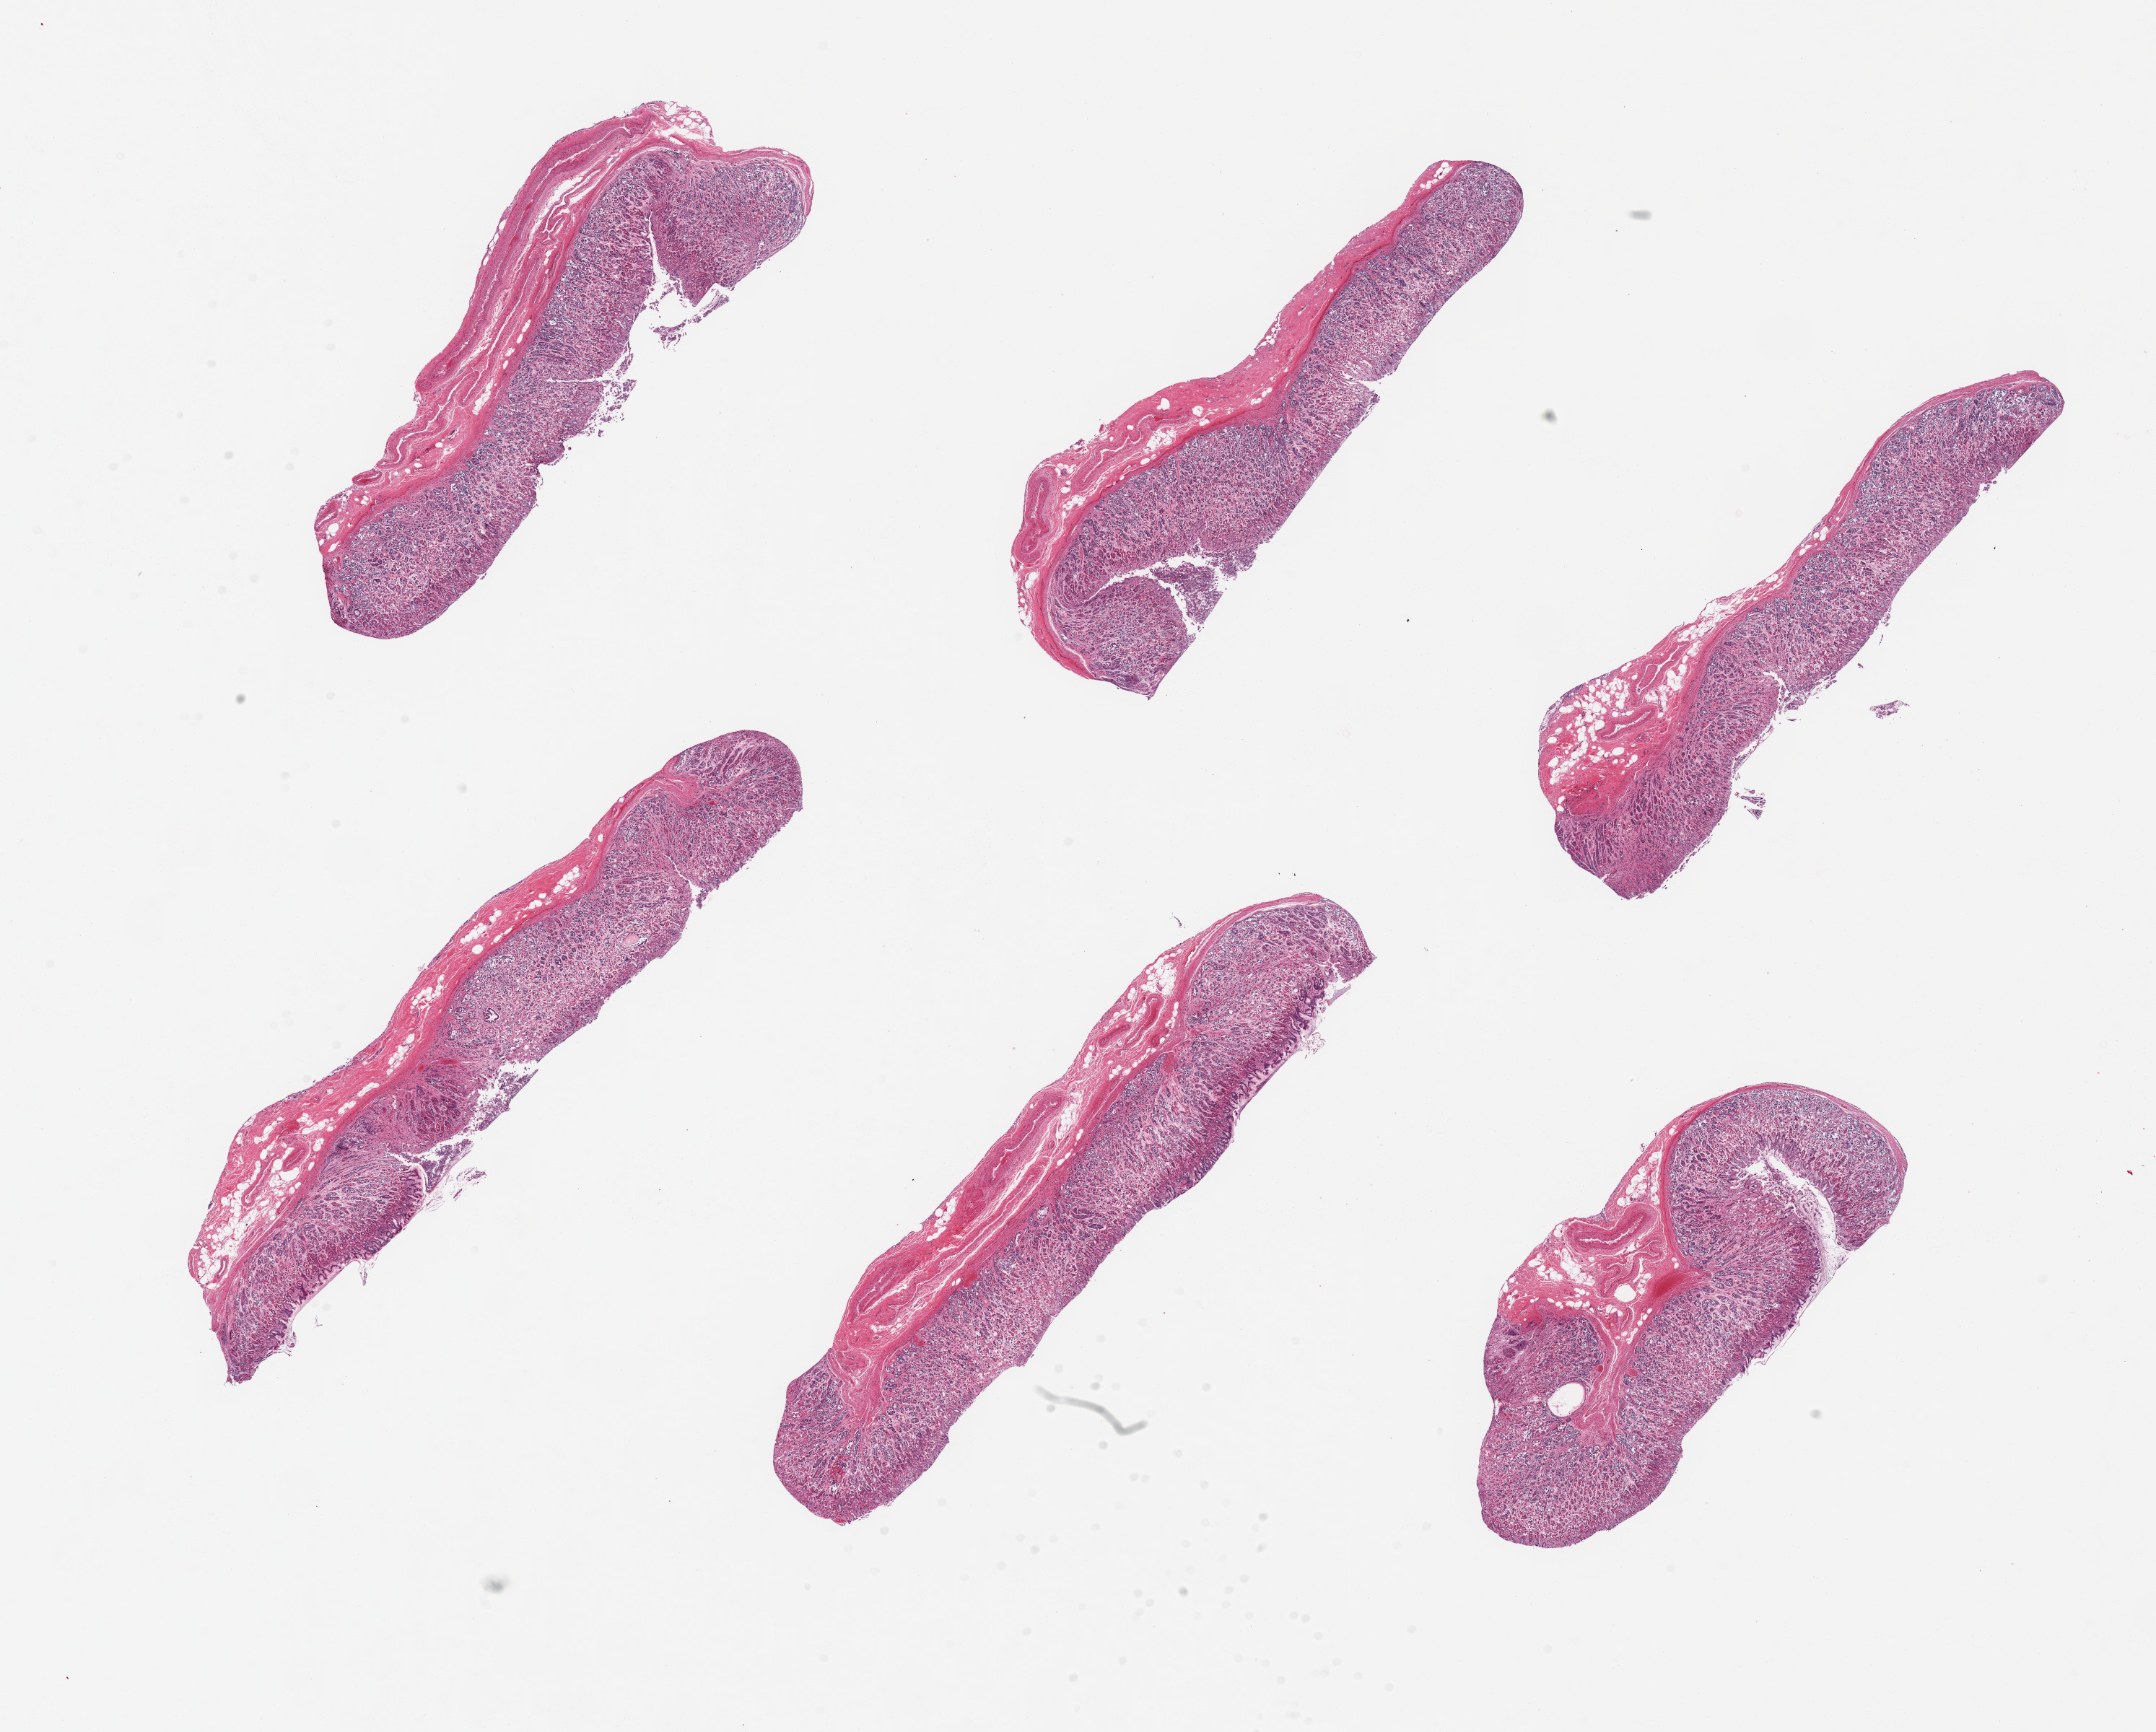
Hematoxylin and eosin (H&E) whole-slide image — a low-resolution overview of the entire scanned area, about 23.6 x 19.0 mm. PAXgene-fixed paraffin-embedded (PFPE) section. Target tissue: stomach. Donor tissue sample.
Reviewer comment on this tissue sample: 6 pieces, mucosa up to ~1mm, 50-70% thickness, moderately-advanced autolysis.